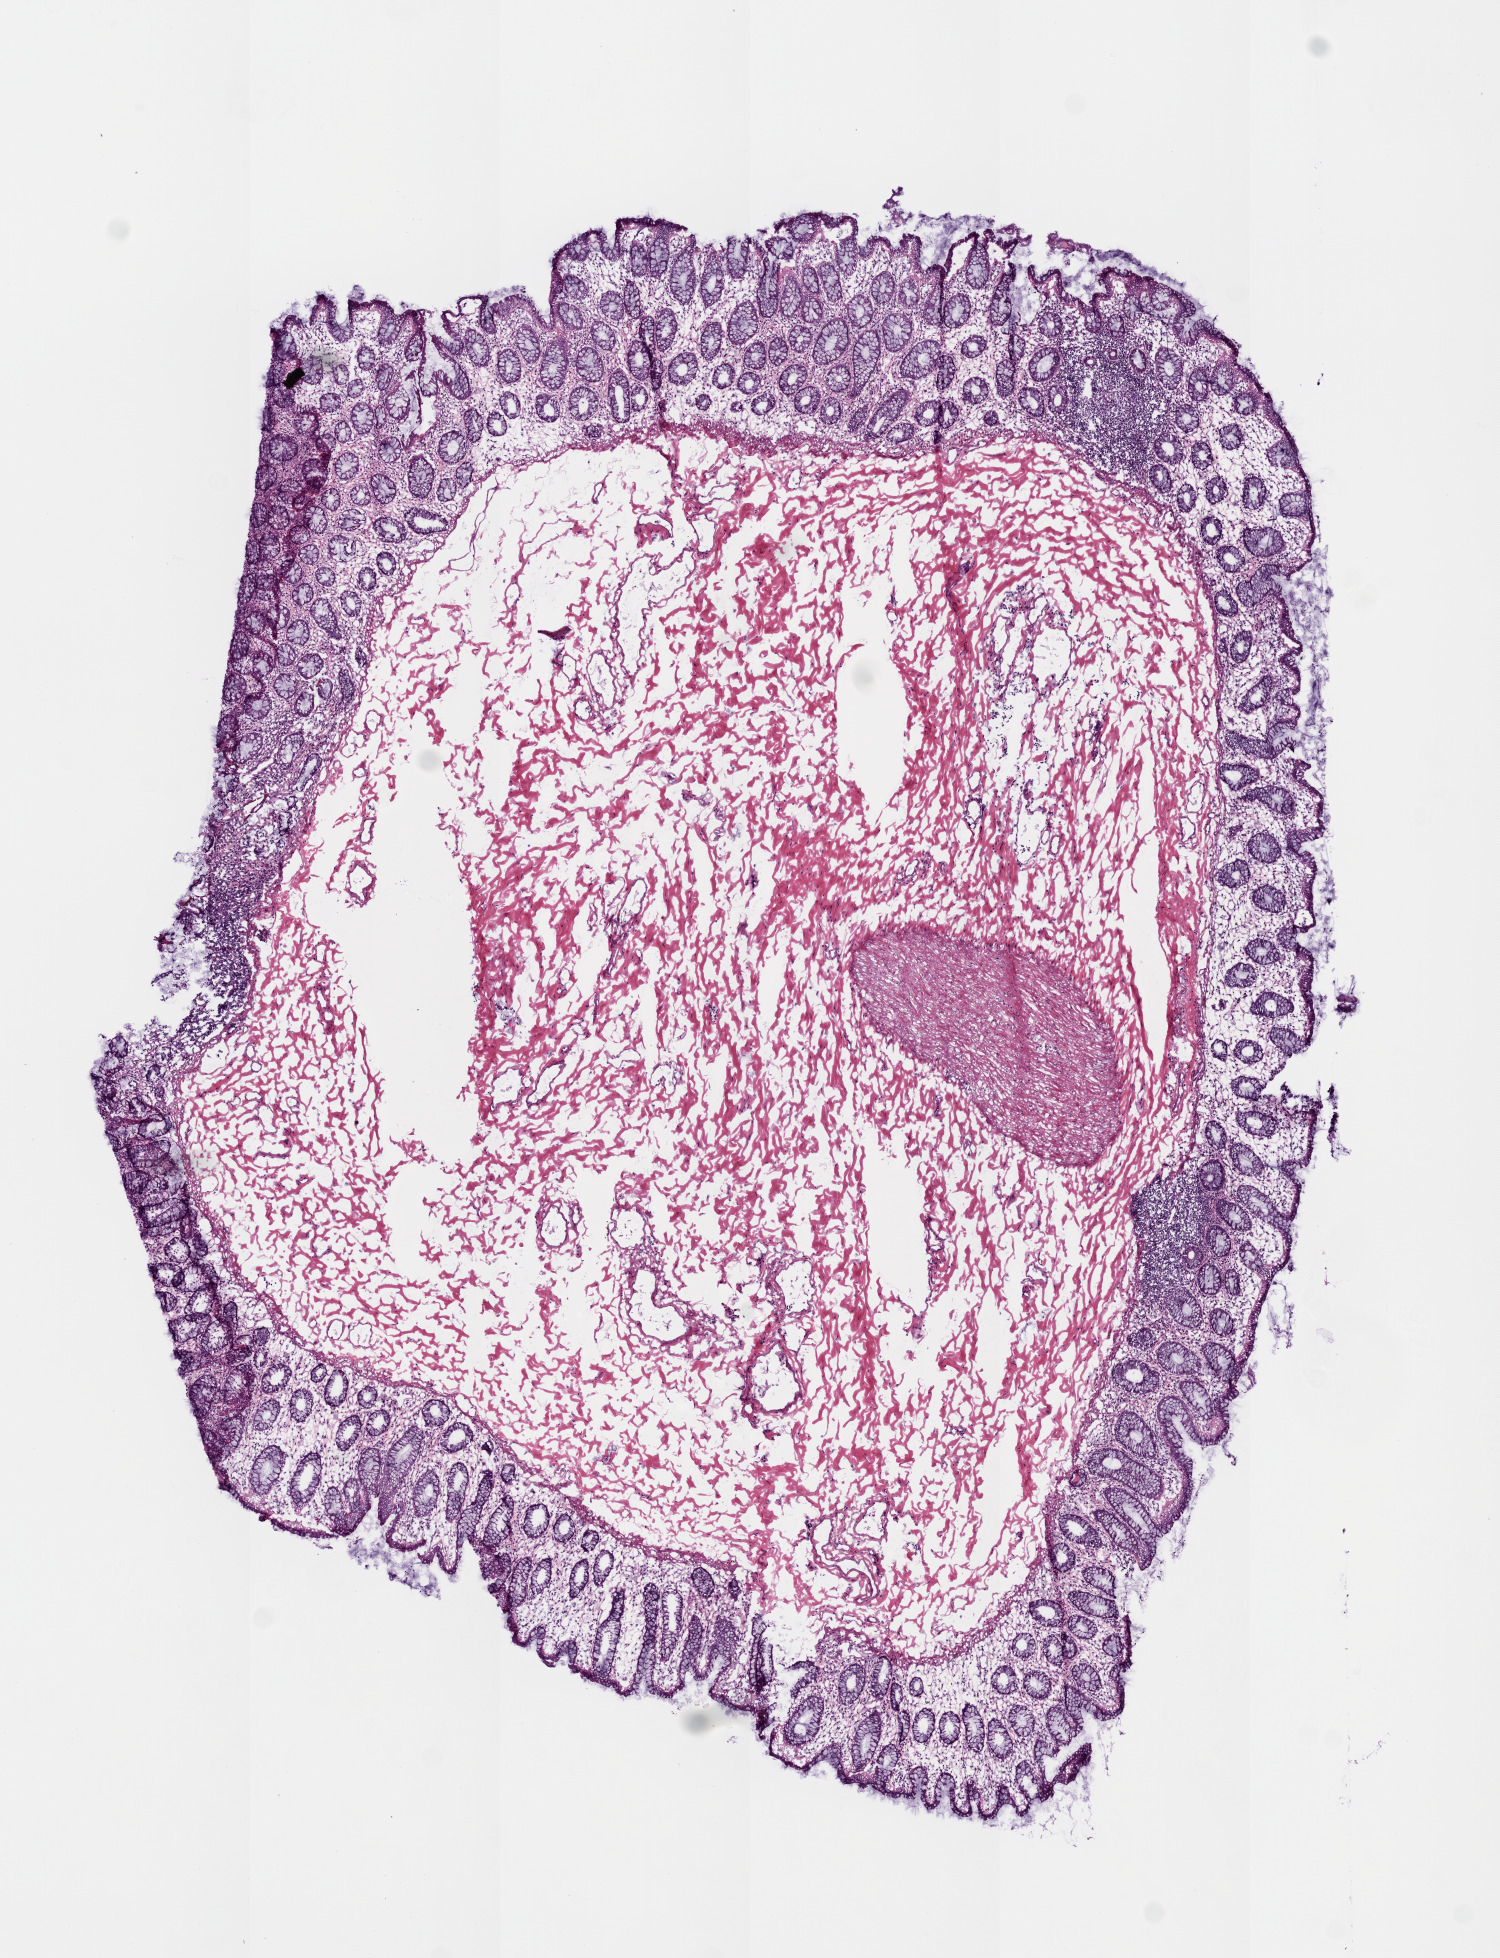
H&E-stained whole-slide image — whole scanned area (about 6.0 x 7.9 mm) shown as a low-resolution overview; frozen section from the top of the tissue portion; colon, solid tissue normal (non-tumour tissue) sample. Male patient; age at initial diagnosis 71 years.
This section: solid tissue normal (non-tumour) sample from the same patient. Patient diagnosis: Mucinous adenocarcinoma (sigmoid colon).